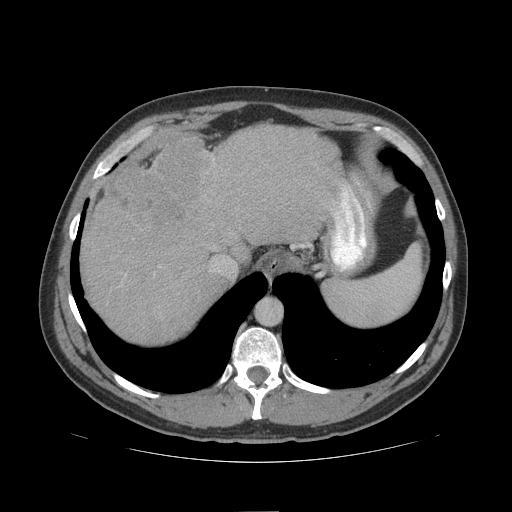
Contrast-enhanced abdominal CT (liver protocol), one axial slice. Position 83 of 109 along the scan axis. Reconstruction kernel STANDARD. 140 kVp. Soft-tissue window (W 400 / L 40 HU). 512 × 512 image matrix, field of view 420 × 420 mm. Case-level facts recorded for this patient, not image findings: diagnosis: hepatocellular carcinoma (patient treated with transarterial chemoembolisation; whether this scan precedes or follows treatment is not stated here); TNM stage (as recorded): Stage-IIIB; Child-Pugh class: A; tumour differentiation: poorly differentiated.
Structures marked on this image (semi-automatically segmented with operator editing):
- abdominal aorta: bounding box <257,299,281,326> (left, top, right, bottom; pixels)
- liver parenchyma outside the tumour (the mass and vessels are separate outlines, so this box may not span the whole liver): <80,124,354,342>
- mass: <109,136,223,234>
- liver vessels: <339,187,353,208>